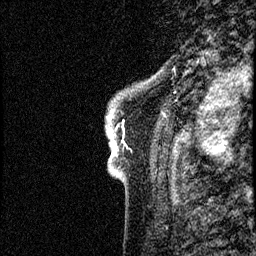
Breast MRI (dynamic contrast-enhanced), one sagittal slice; slice 4 of 60 in the series (ordered by position); dynamic contrast-enhanced study with each time point stored as its own series, time point 2 of 4 at this slice position (early post-contrast, ordered by acquisition time); 1.5 T; TE 4.2 ms, TR 17.6 ms; 256 × 256 image matrix, field of view 200 × 200 mm. Patient: female, 40 years. Case-level facts recorded for this patient, not image findings: setting: breast cancer imaged before/during neoadjuvant chemotherapy; receptor status: HER2-positive.
Outlined on this slice (semi-automatic segmentation, software-assisted and operator-edited):
- analysis volume of interest (the breast-tissue region the enhancement analysis was run in; not a lesion): bounding box [x1, y1, x2, y2] px = [101, 55, 185, 206]
- tumour enhancement mask (voxels above the 100 % enhancement threshold inside the analysis volume of interest): [108, 115, 117, 155]